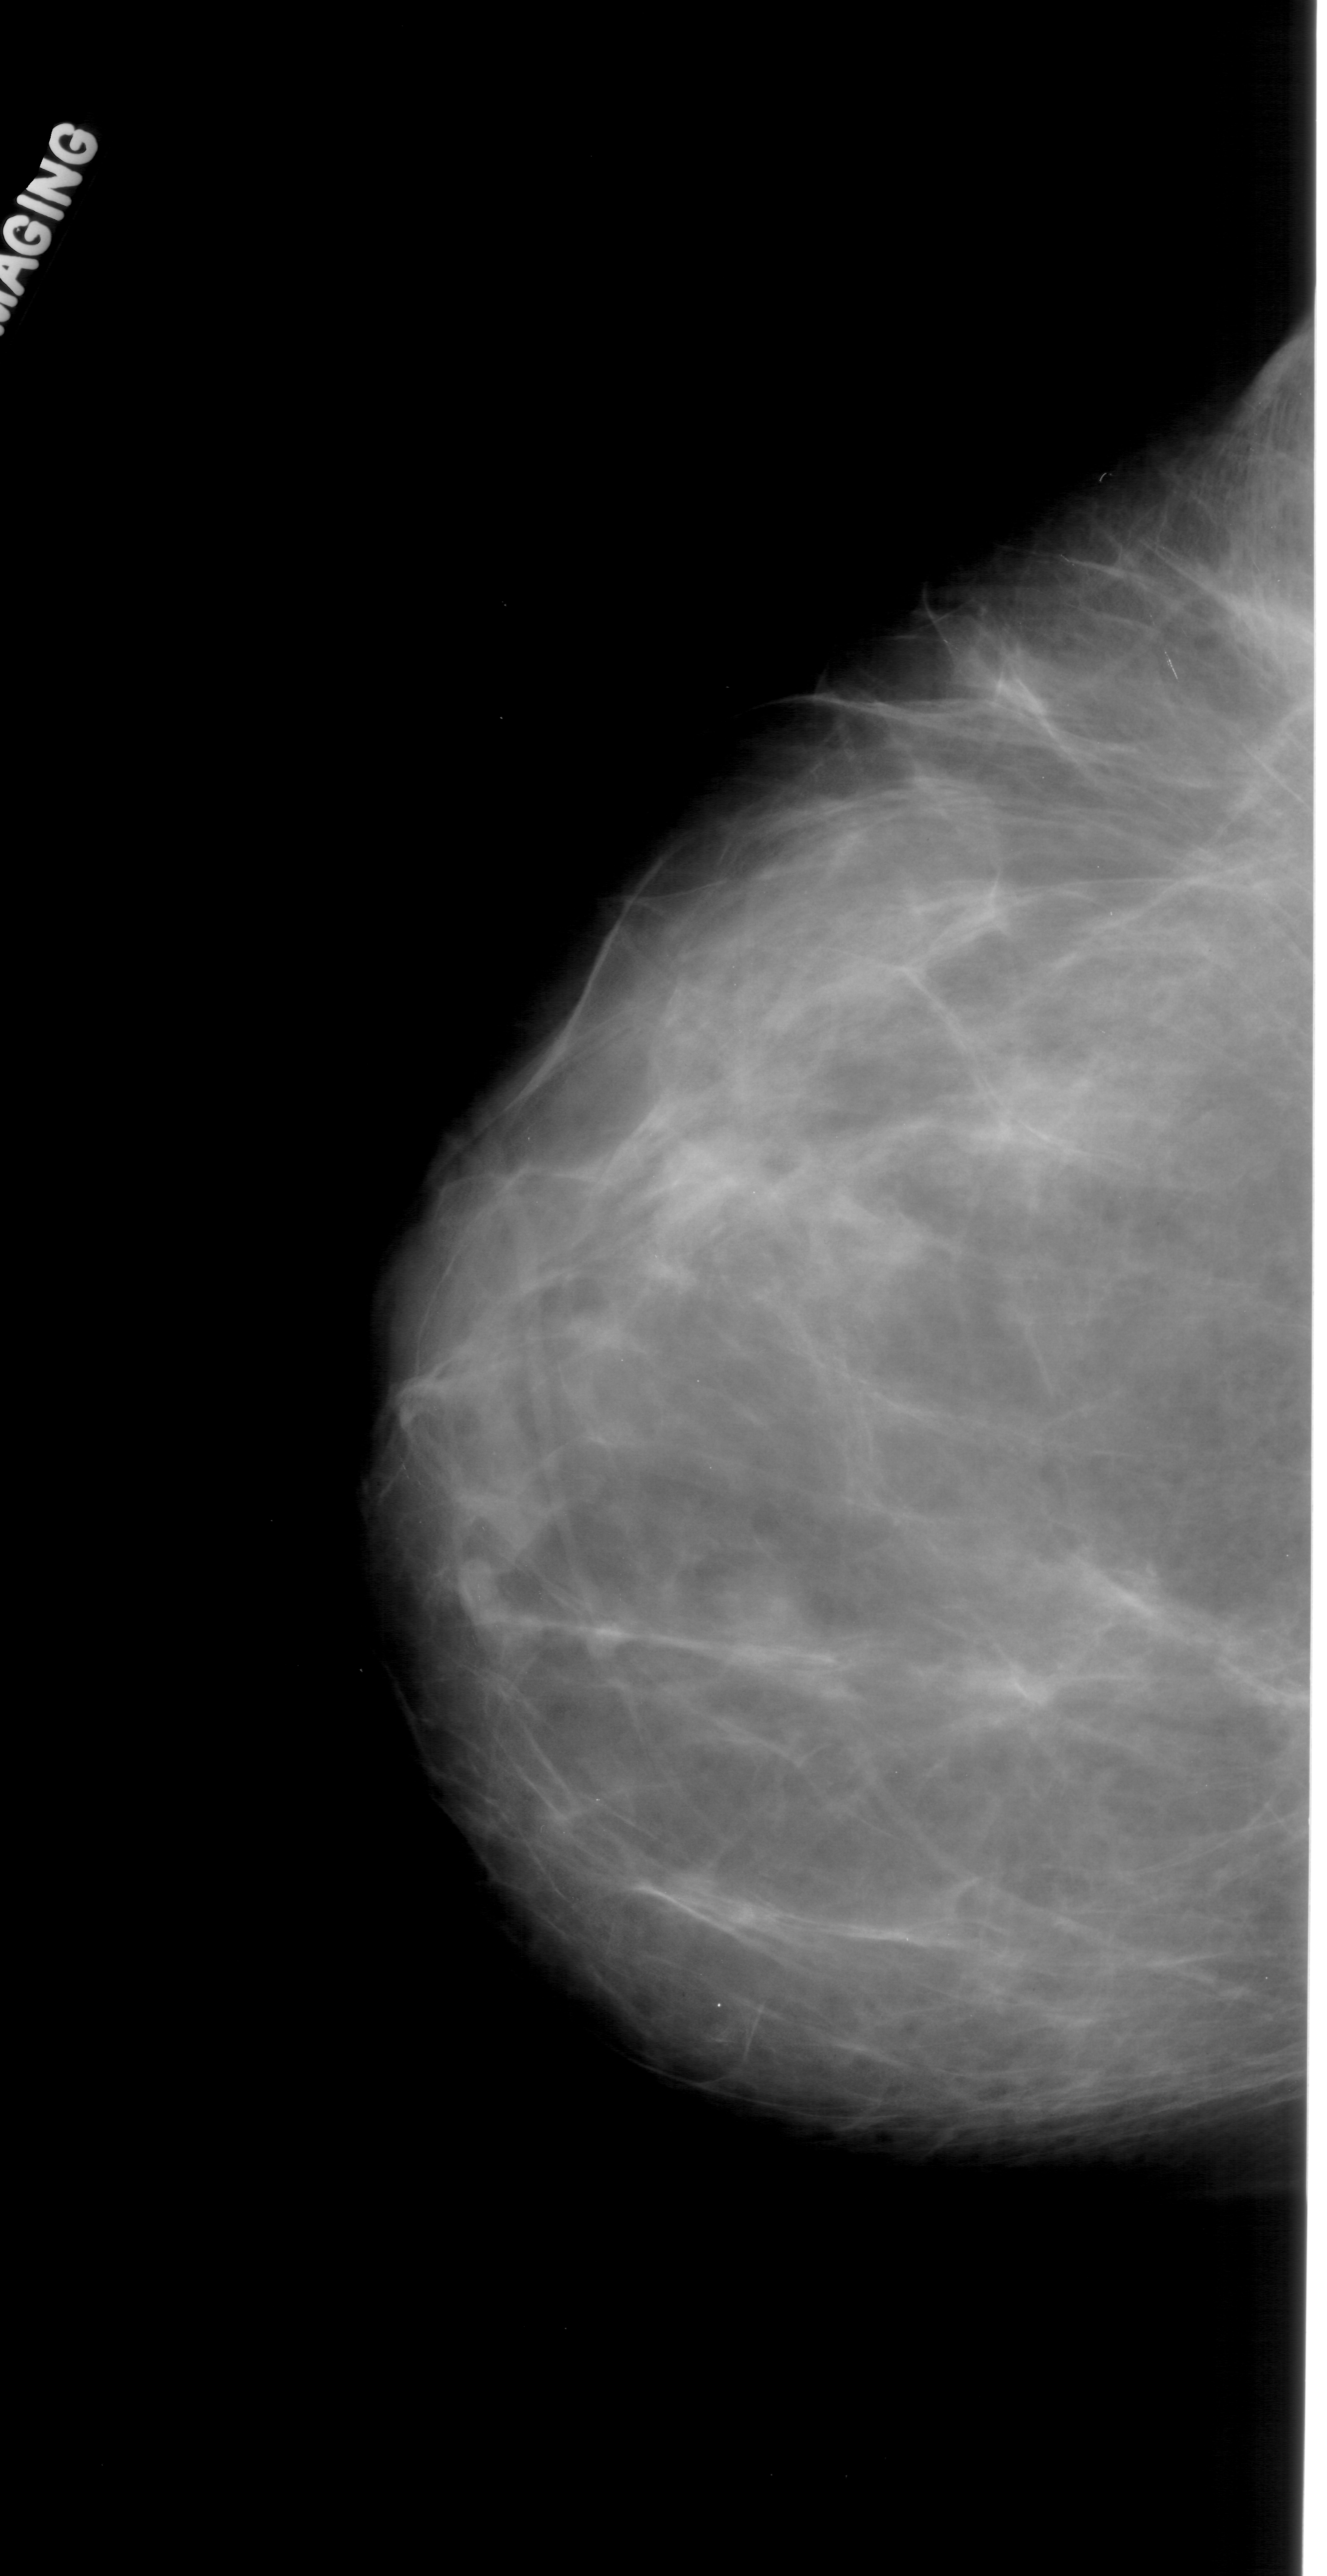
Scanned film-screen mammogram; left breast; craniocaudal (CC) view; BI-RADS breast density category 1 (scale 1–4).
- Mass, shape lobulated, margins circumscribed; BI-RADS assessment category 4; pathology result (as recorded, not read from the image): benign.